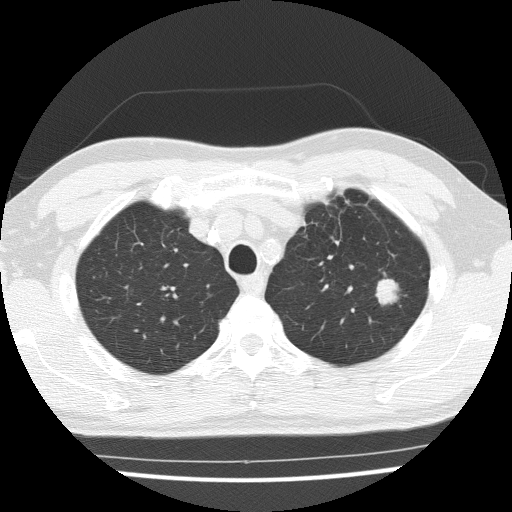
Low-dose screening chest CT, axial slice. Third screening round (two years after baseline). Lung window (W 1500 / L -600 HU). 2 mm slice thickness. Lung (sharp) reconstruction kernel (FC51). Slice 36 of 154 in the series. Male participant, aged 65 years at enrolment.
- Expert reader's lesion annotation, bounding box (x1, y1, x2, y2) in pixels: (356, 270, 409, 316).
- The exam's reader record, not a measurement of the box and not confirmed to be the same lesion: non-calcified nodule or mass ≥4 mm, left upper lobe, 16 × 15 mm, poorly defined margins, soft tissue attenuation, pre-existing on the prior screen: yes; interval growth: yes.
- Participant outcome: lung cancer diagnosed 42 days after this screen — squamous cell carcinoma, NOS, left upper lobe, moderately differentiated (G2), stage IA (AJCC 6th edition), 25 mm at pathology.